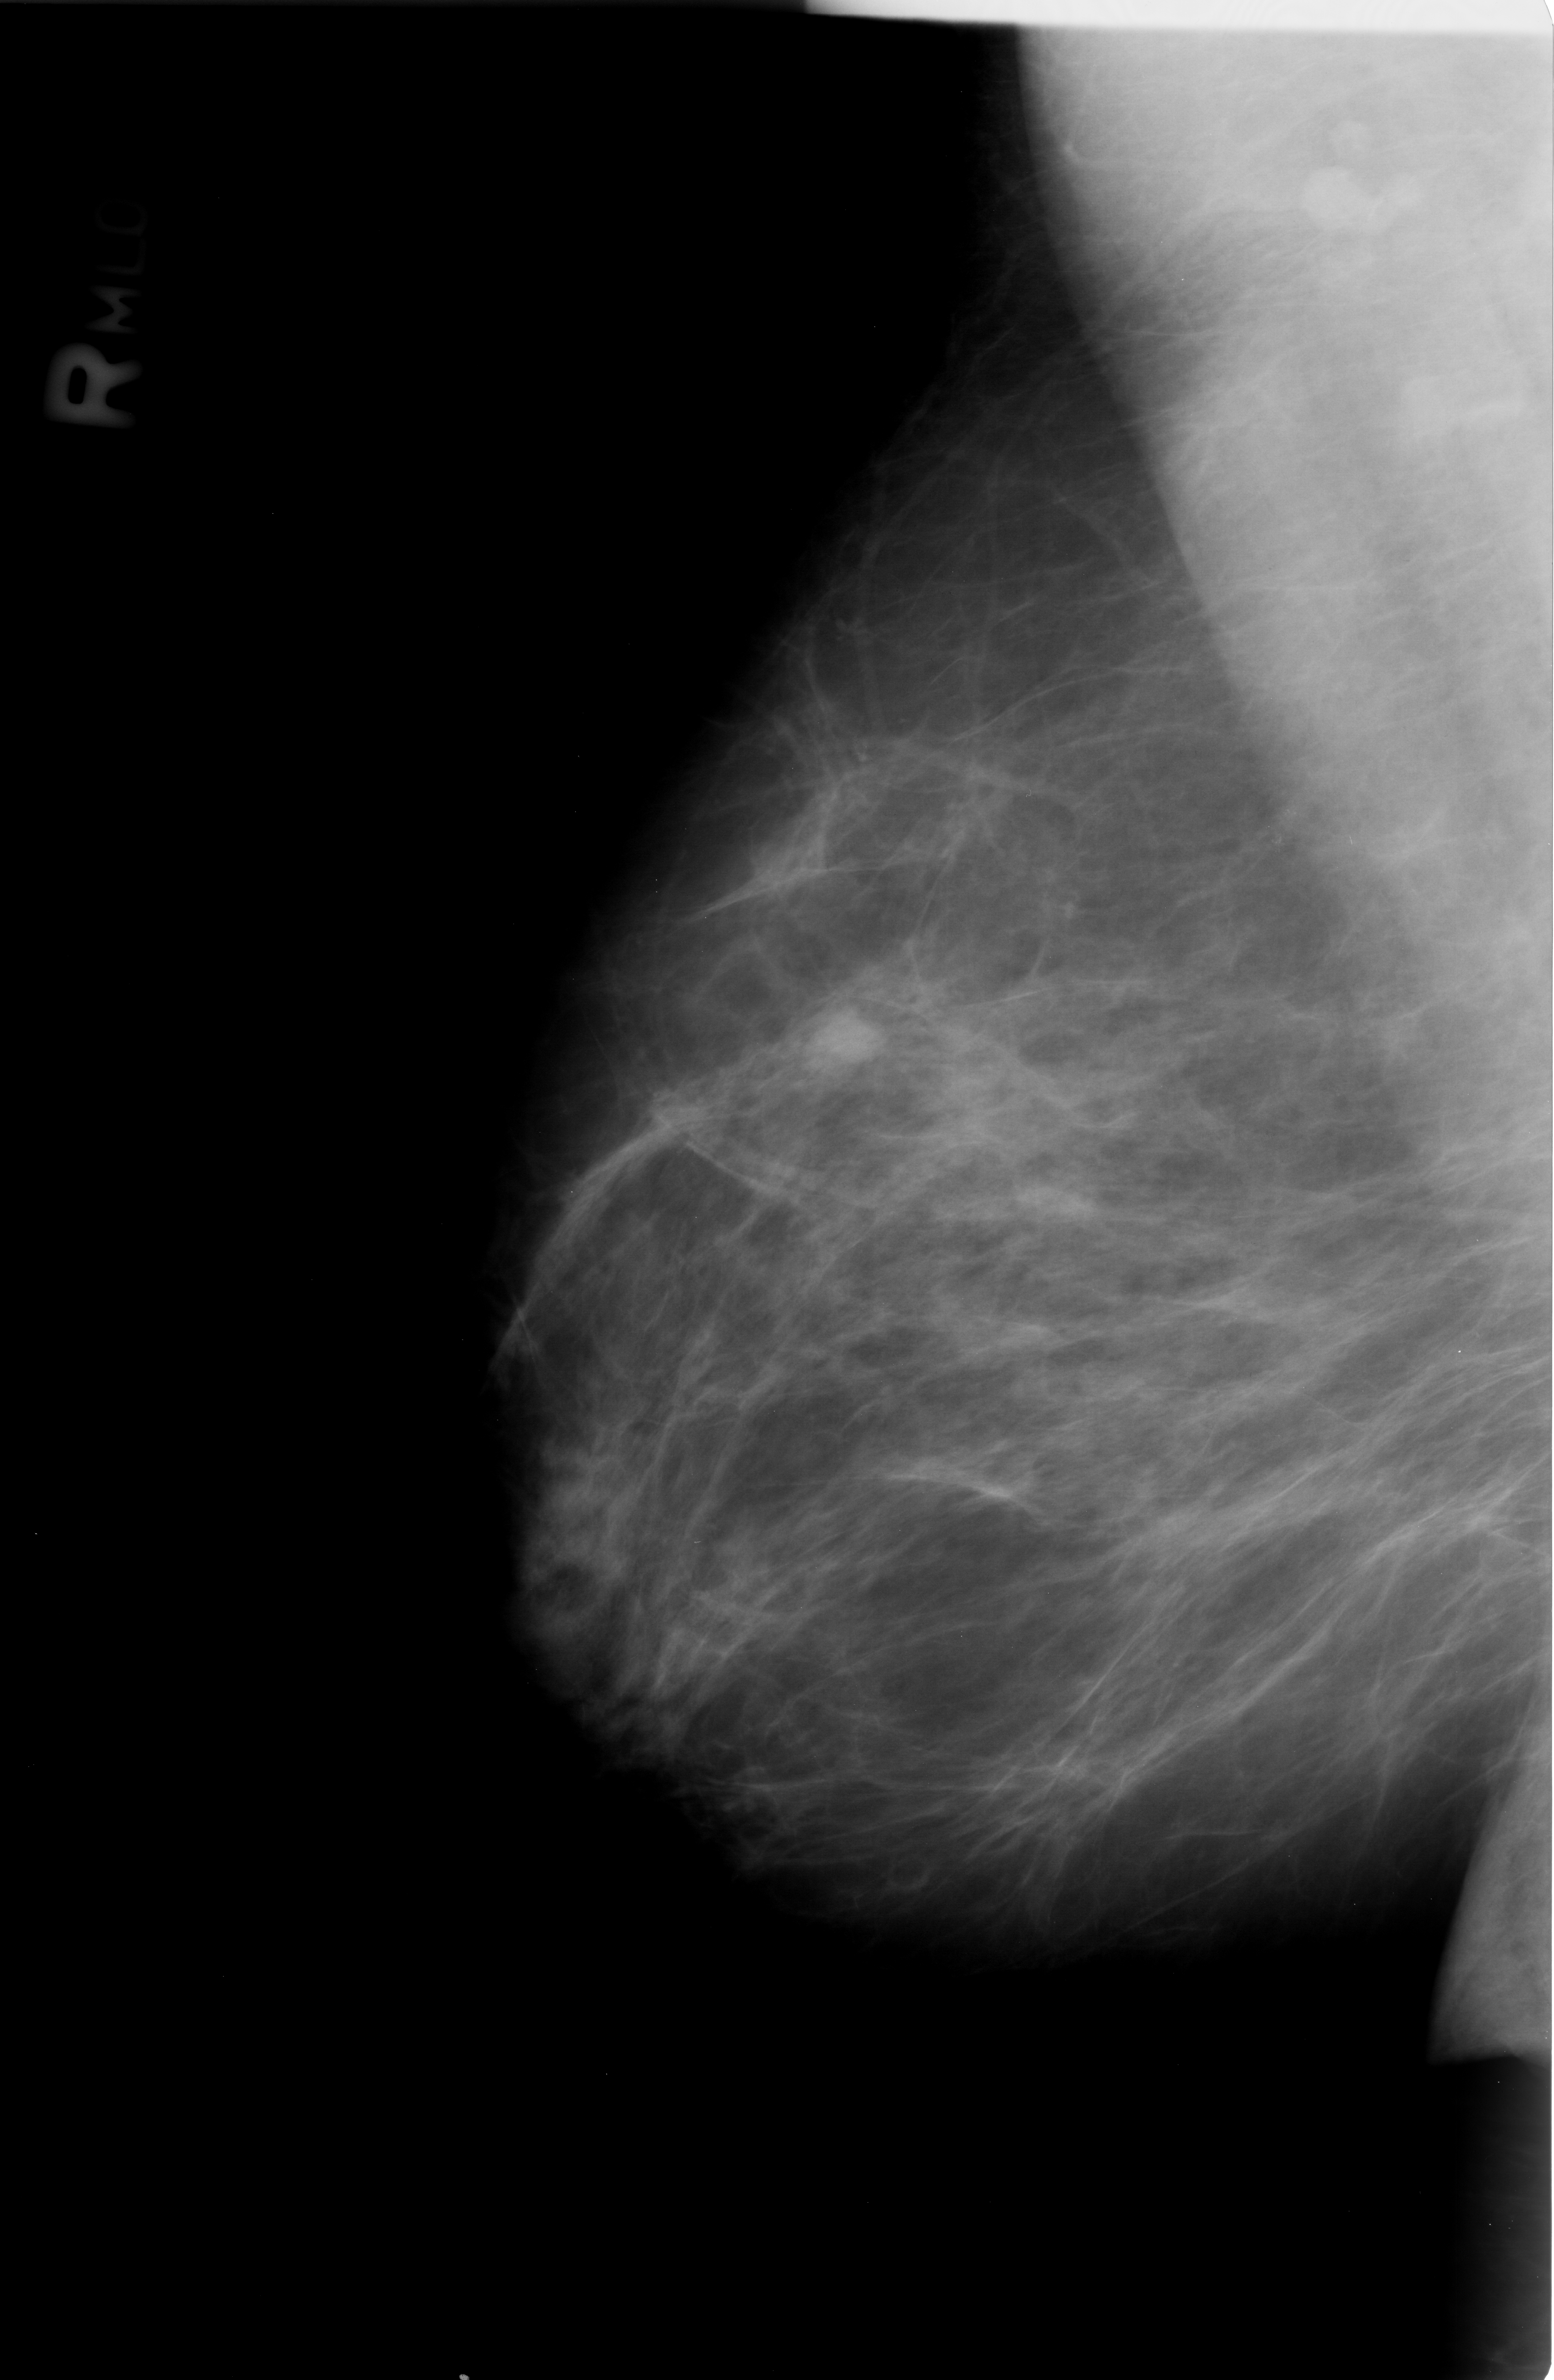
Scanned film-screen mammogram; right breast; MLO view; BI-RADS breast density category 2 (scale 1–4); 1554 × 2380 image matrix.
Marked abnormalities (boxes around the expert regions of interest):
- mass, shape lobulated, margins circumscribed / obscured; BI-RADS assessment category 4; pathology result (as recorded, not read from the image): benign: bounding box <803,998,888,1072> (left, top, right, bottom; pixels)